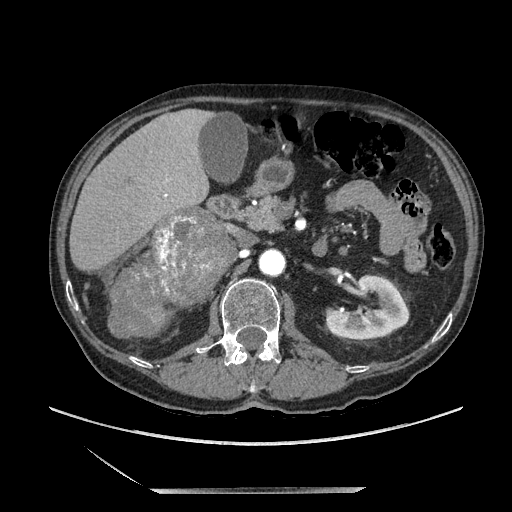
Contrast-enhanced abdominal CT, one axial slice; position 104 of 243 along the scan axis; soft-tissue window (W 400 / L 40 HU); 1.25 mm slice thickness; 512 × 512 image matrix, field of view 420 × 420 mm. Male patient. From the clinical record (not read from this slice): diagnosis: adrenocortical carcinoma; tumour side: right adrenal; tumour size at pathology: 16 cm.
Structures marked on this image (semi-automatically segmented with operator editing):
- mass: bounding box (x1, y1, x2, y2) in pixels: (112, 208, 229, 337)